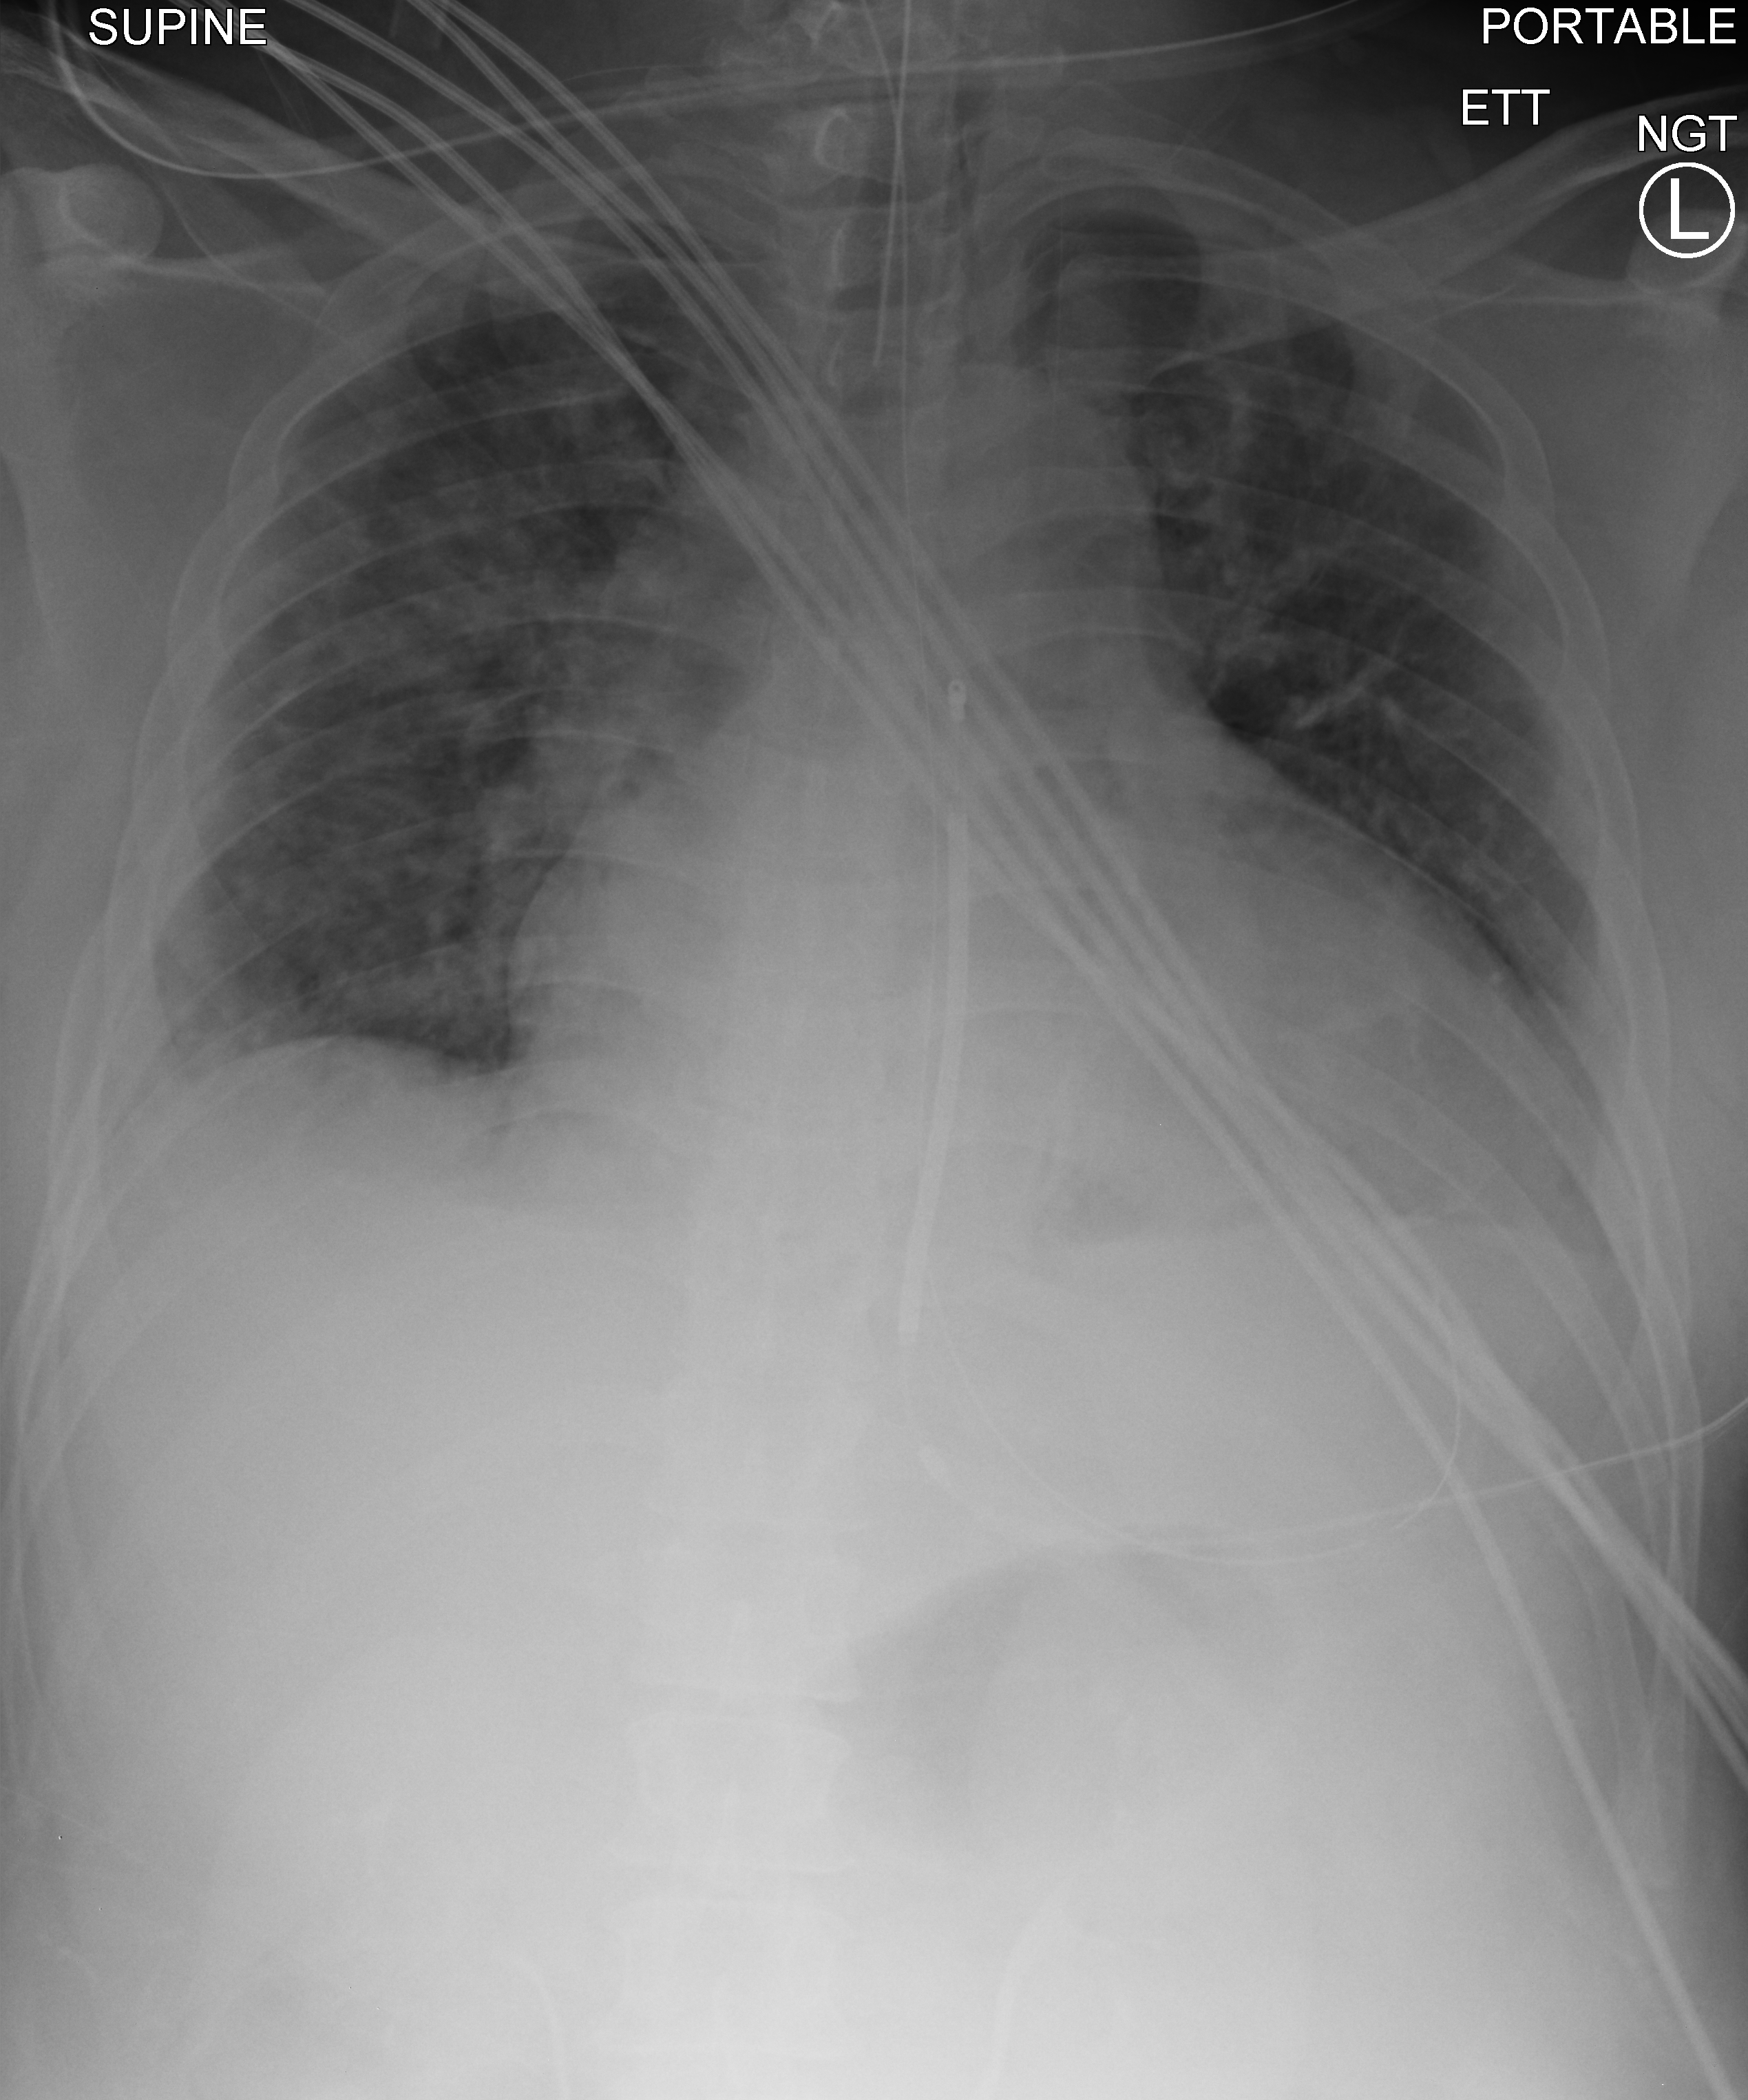
Bedside chest radiograph (computed radiography); anteroposterior (AP) projection. Patient hospitalised with COVID-19; male, aged 18–59 years.
Admission-level facts for this patient (not findings on this image; timing relative to this image not recorded): admitted to intensive care during this hospital stay: no.